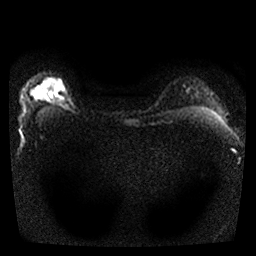
Breast MRI, one axial slice. Position 25 of 25 along the scan axis. Diffusion-weighted series; image 2 of 4 stored at this slice position (different b-values; order by instance number). 1.5 T. 4 mm slice thickness. 256 × 256 image matrix, field of view 300 × 300 mm. Female patient.
Structures marked on this image (manually delineated by an expert):
- tumour on diffusion-weighted imaging: bounding box <53,83,63,98> (left, top, right, bottom; pixels)